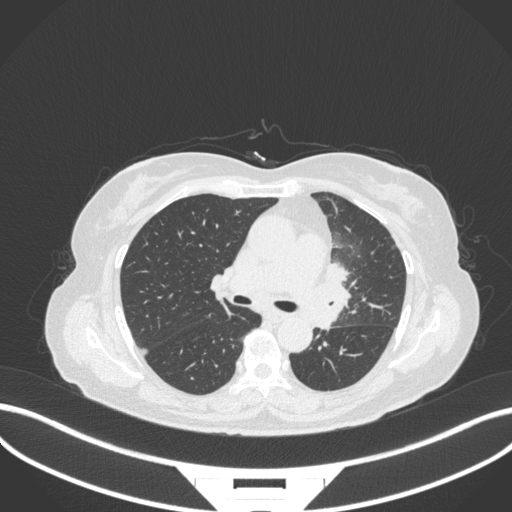
Chest CT, one axial slice; position 201 of 382 along the scan axis; reconstruction kernel B31f; 120 kVp; lung window (W 1500 / L -600 HU); 512 × 512 image matrix, field of view 400 × 400 mm. Female patient, age 64 years. From the clinical record (not read from this slice): clinical TNM (as recorded): T2a N2 M0.
Structures marked on this image (bounding box drawn by a radiologist):
- lung tumour (recorded histology: adenocarcinoma): box from (x=312, y=261) to (x=359, y=332) px